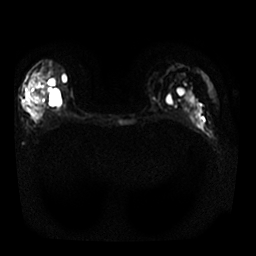
Breast MRI, one axial slice; position 15 of 30 along the scan axis; diffusion-weighted series; image 2 of 4 stored at this slice position (different b-values; order by instance number); 1.5 T; 4 mm slice thickness; 256 × 256 image matrix, field of view 340 × 340 mm. Female patient.
Structures marked on this image (outlined manually by an expert reader):
- tumour on diffusion-weighted imaging: box from (x=29, y=70) to (x=44, y=113) px